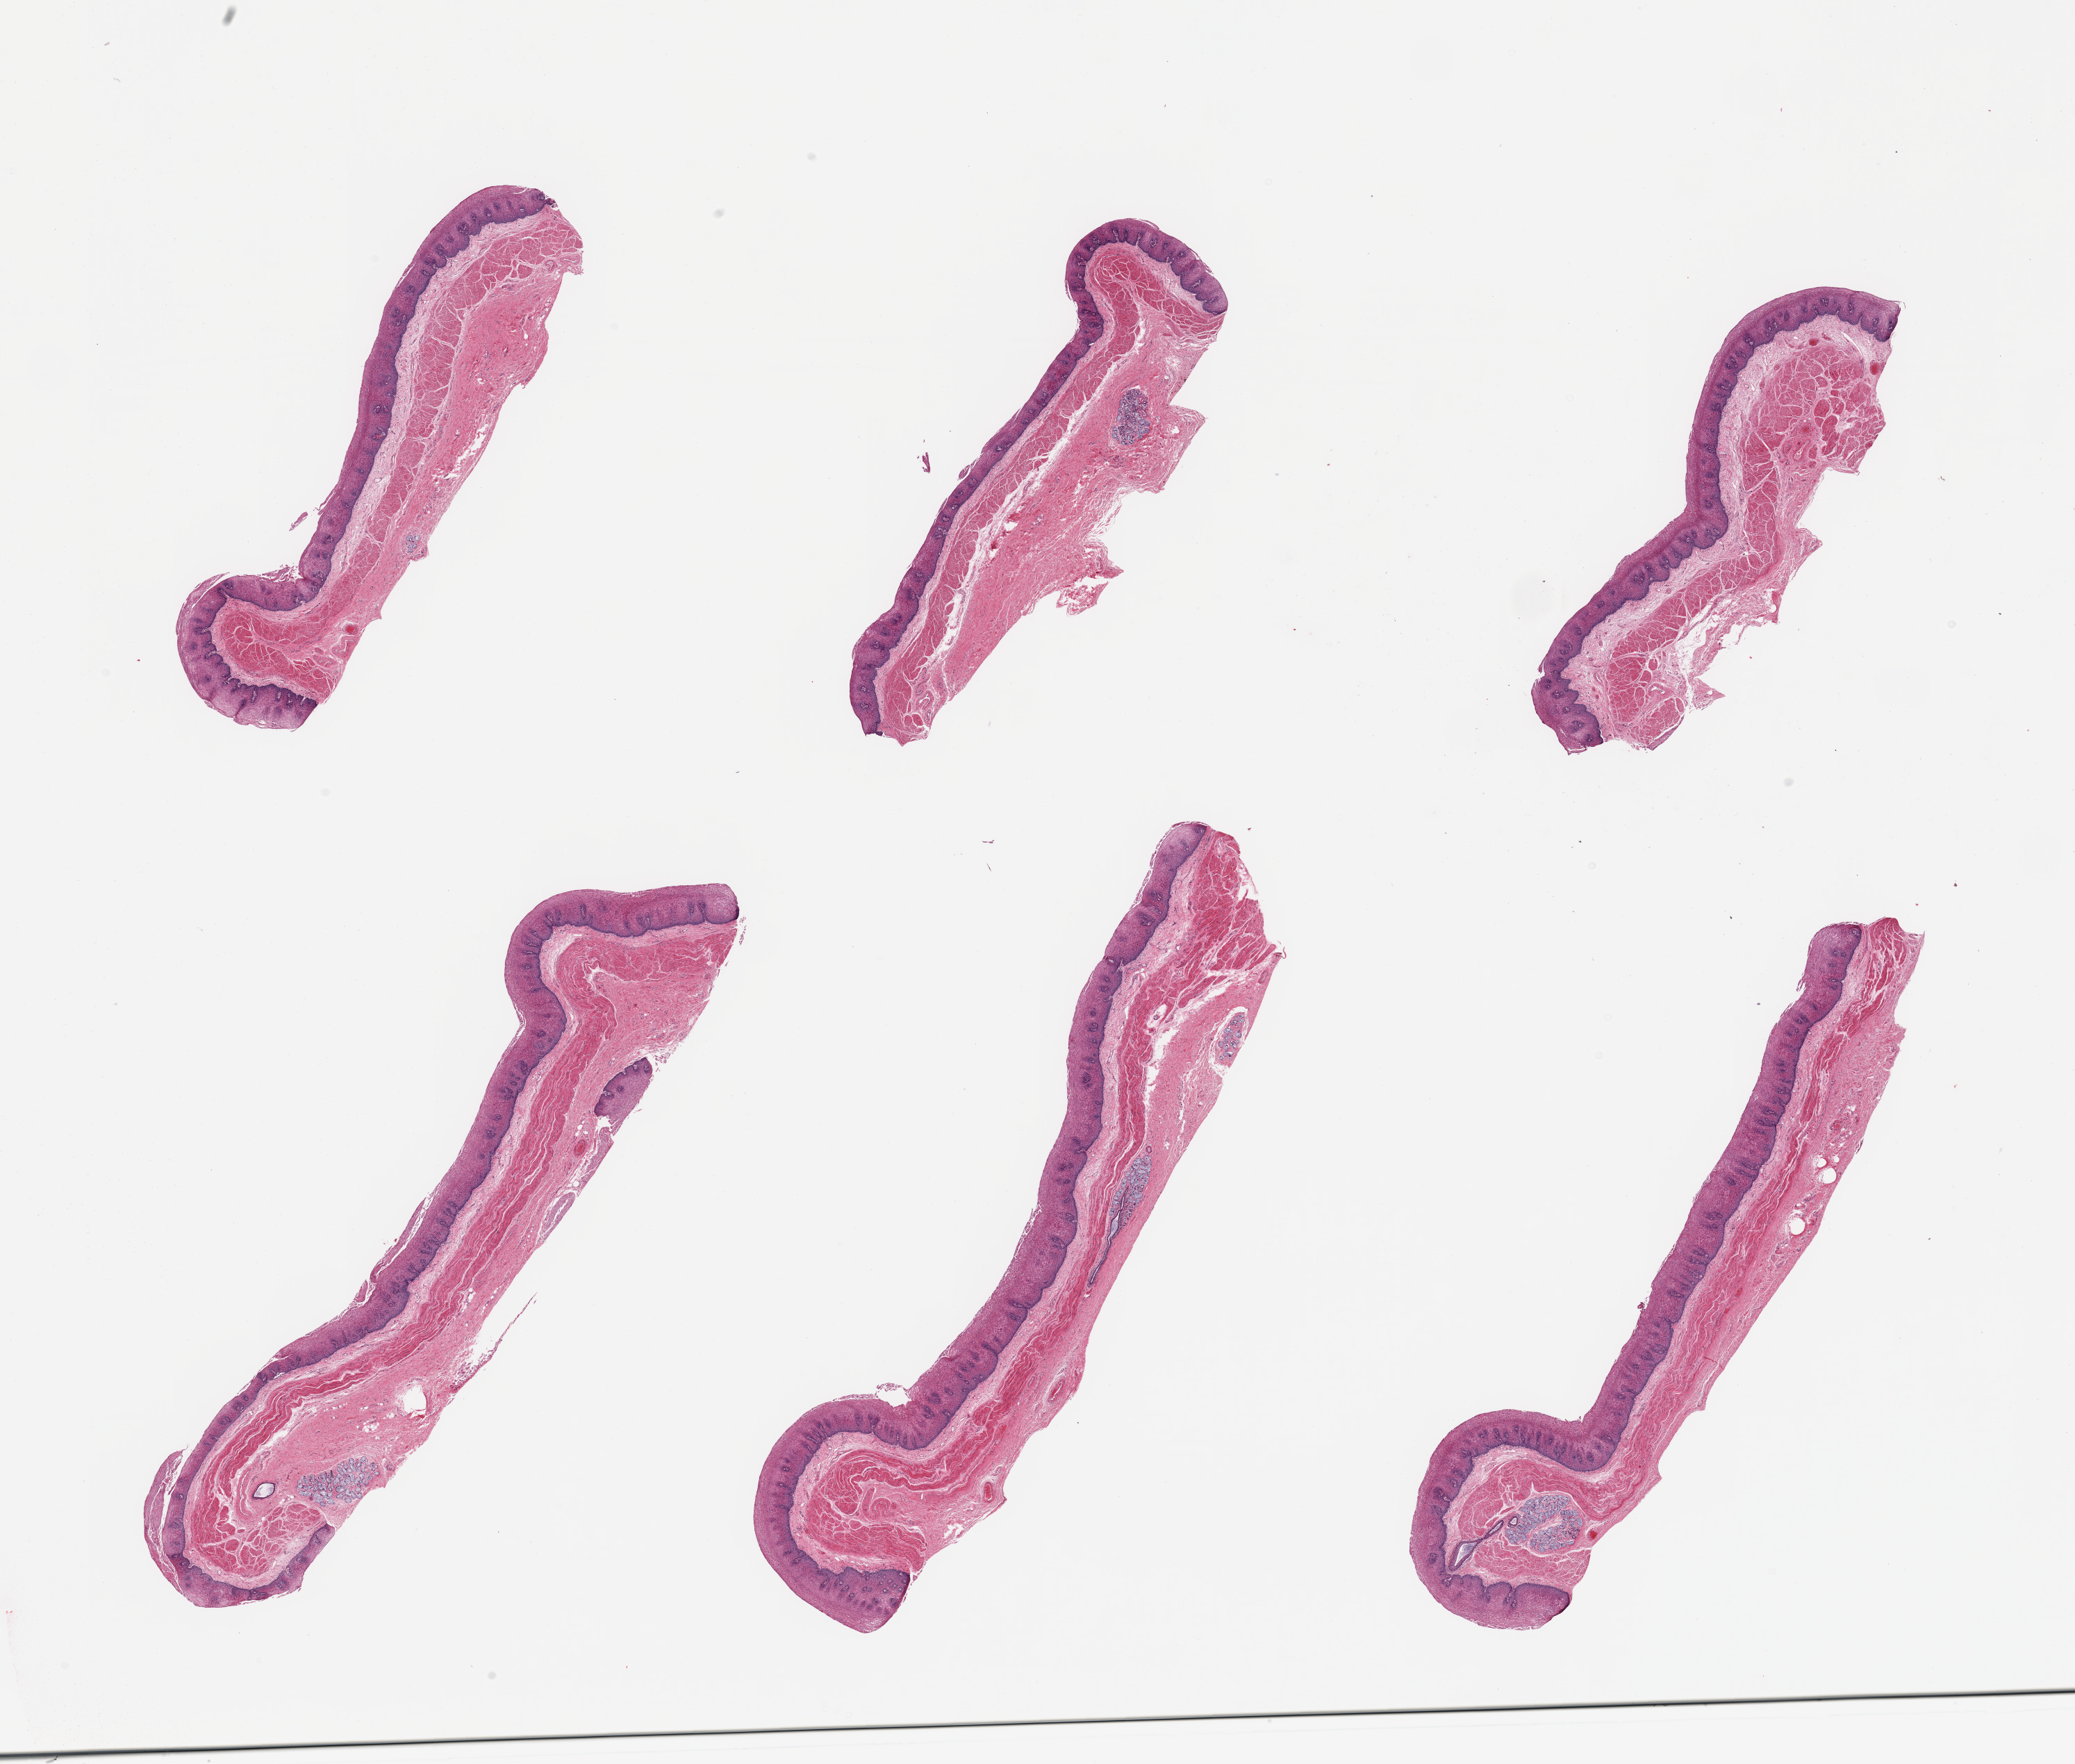
Digitized hematoxylin and eosin (H&E)-stained section, low-resolution overview of the scanned area, about 23.6 x 20.1 mm; PAXgene-fixed, paraffin-embedded tissue; sampled site (target tissue): esophageal mucous membrane; tissue donor sample. Male donor.
* pathologist's review note for this sample: 6 pieces; squamous mucosa up to 0.4mm; submucosal glands